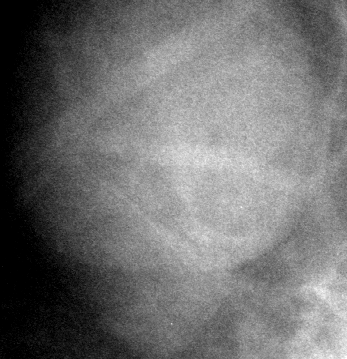
Region of interest cut from a scanned film mammogram (one marked finding); right breast; MLO view; BI-RADS breast density category 3 (scale 1–4).
- Mass, shape lobulated, margins circumscribed; BI-RADS assessment category 3; subtlety rating 4 on a 1 (subtle) to 5 (obvious) scale; pathology (as recorded): benign.